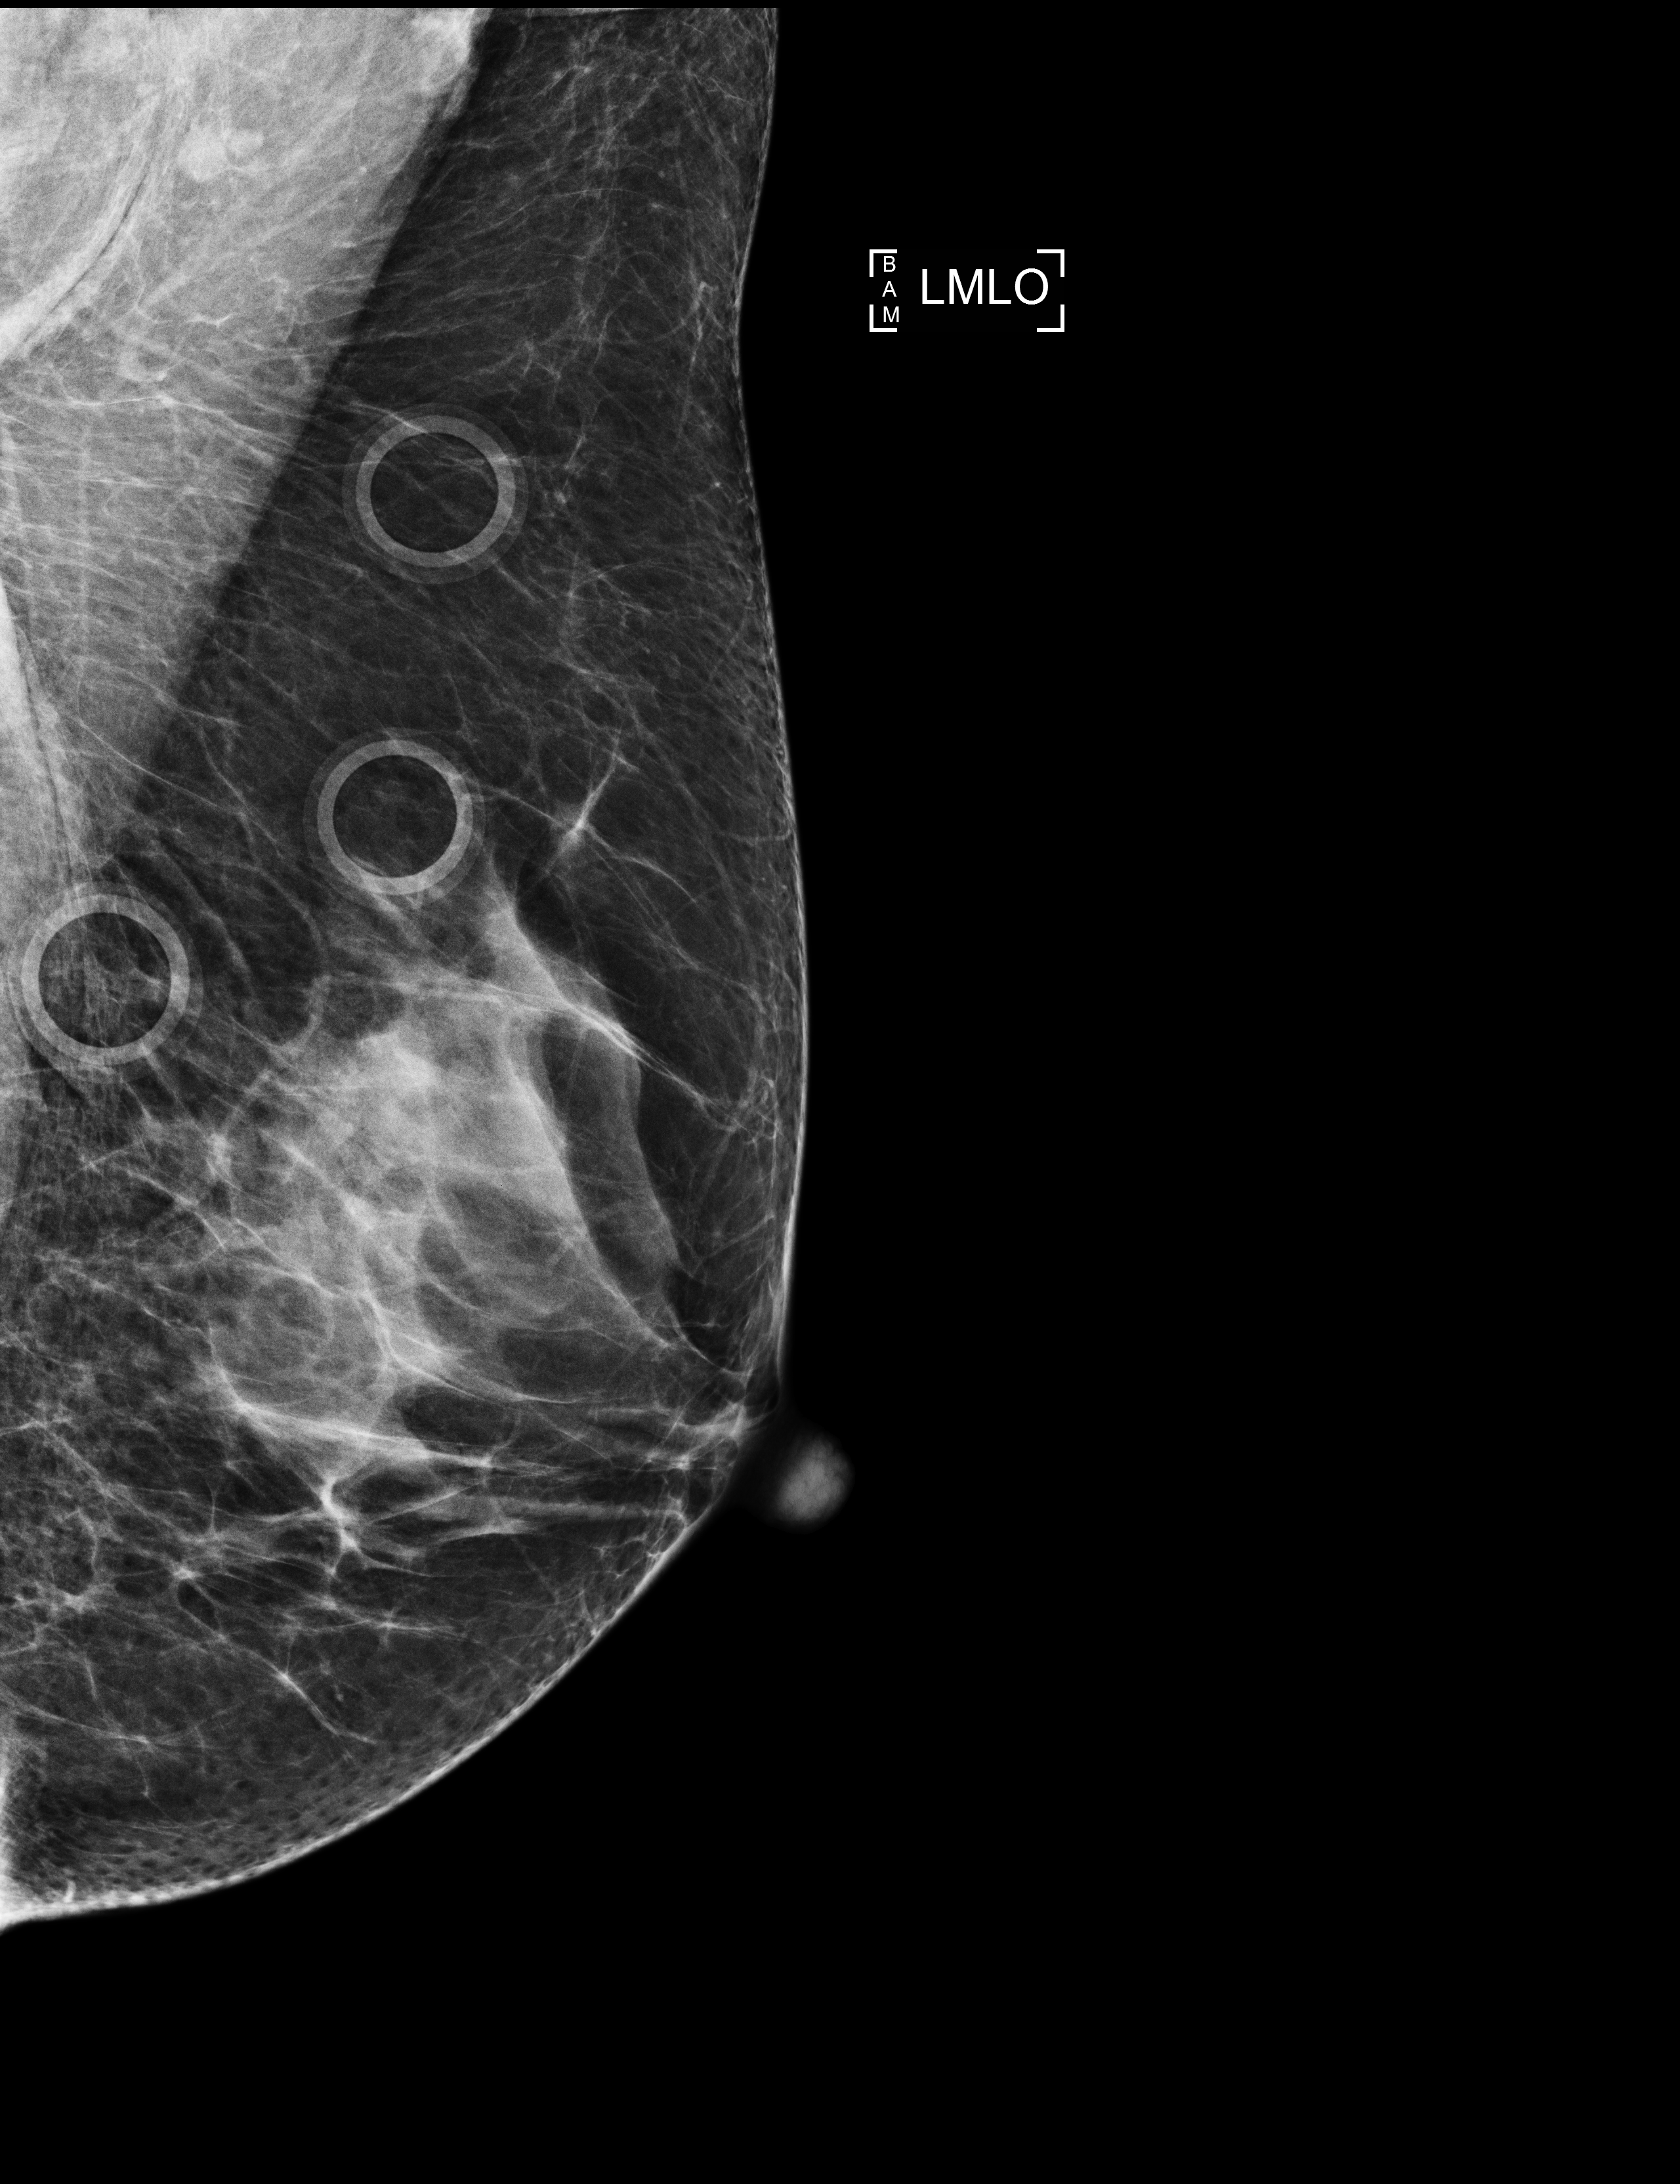
Full-field digital mammogram (FFDM), left breast, MLO view, screening examination, compressed breast thickness 59 mm, system: Selenia Dimensions. Patient aged 59 years (female).
BI-RADS breast density category at the screening exam (both breasts, scale 1–4): 3. Final BI-RADS category for the screening round (tomosynthesis exam, both breasts): category 1. Recall: no recall after this screen.